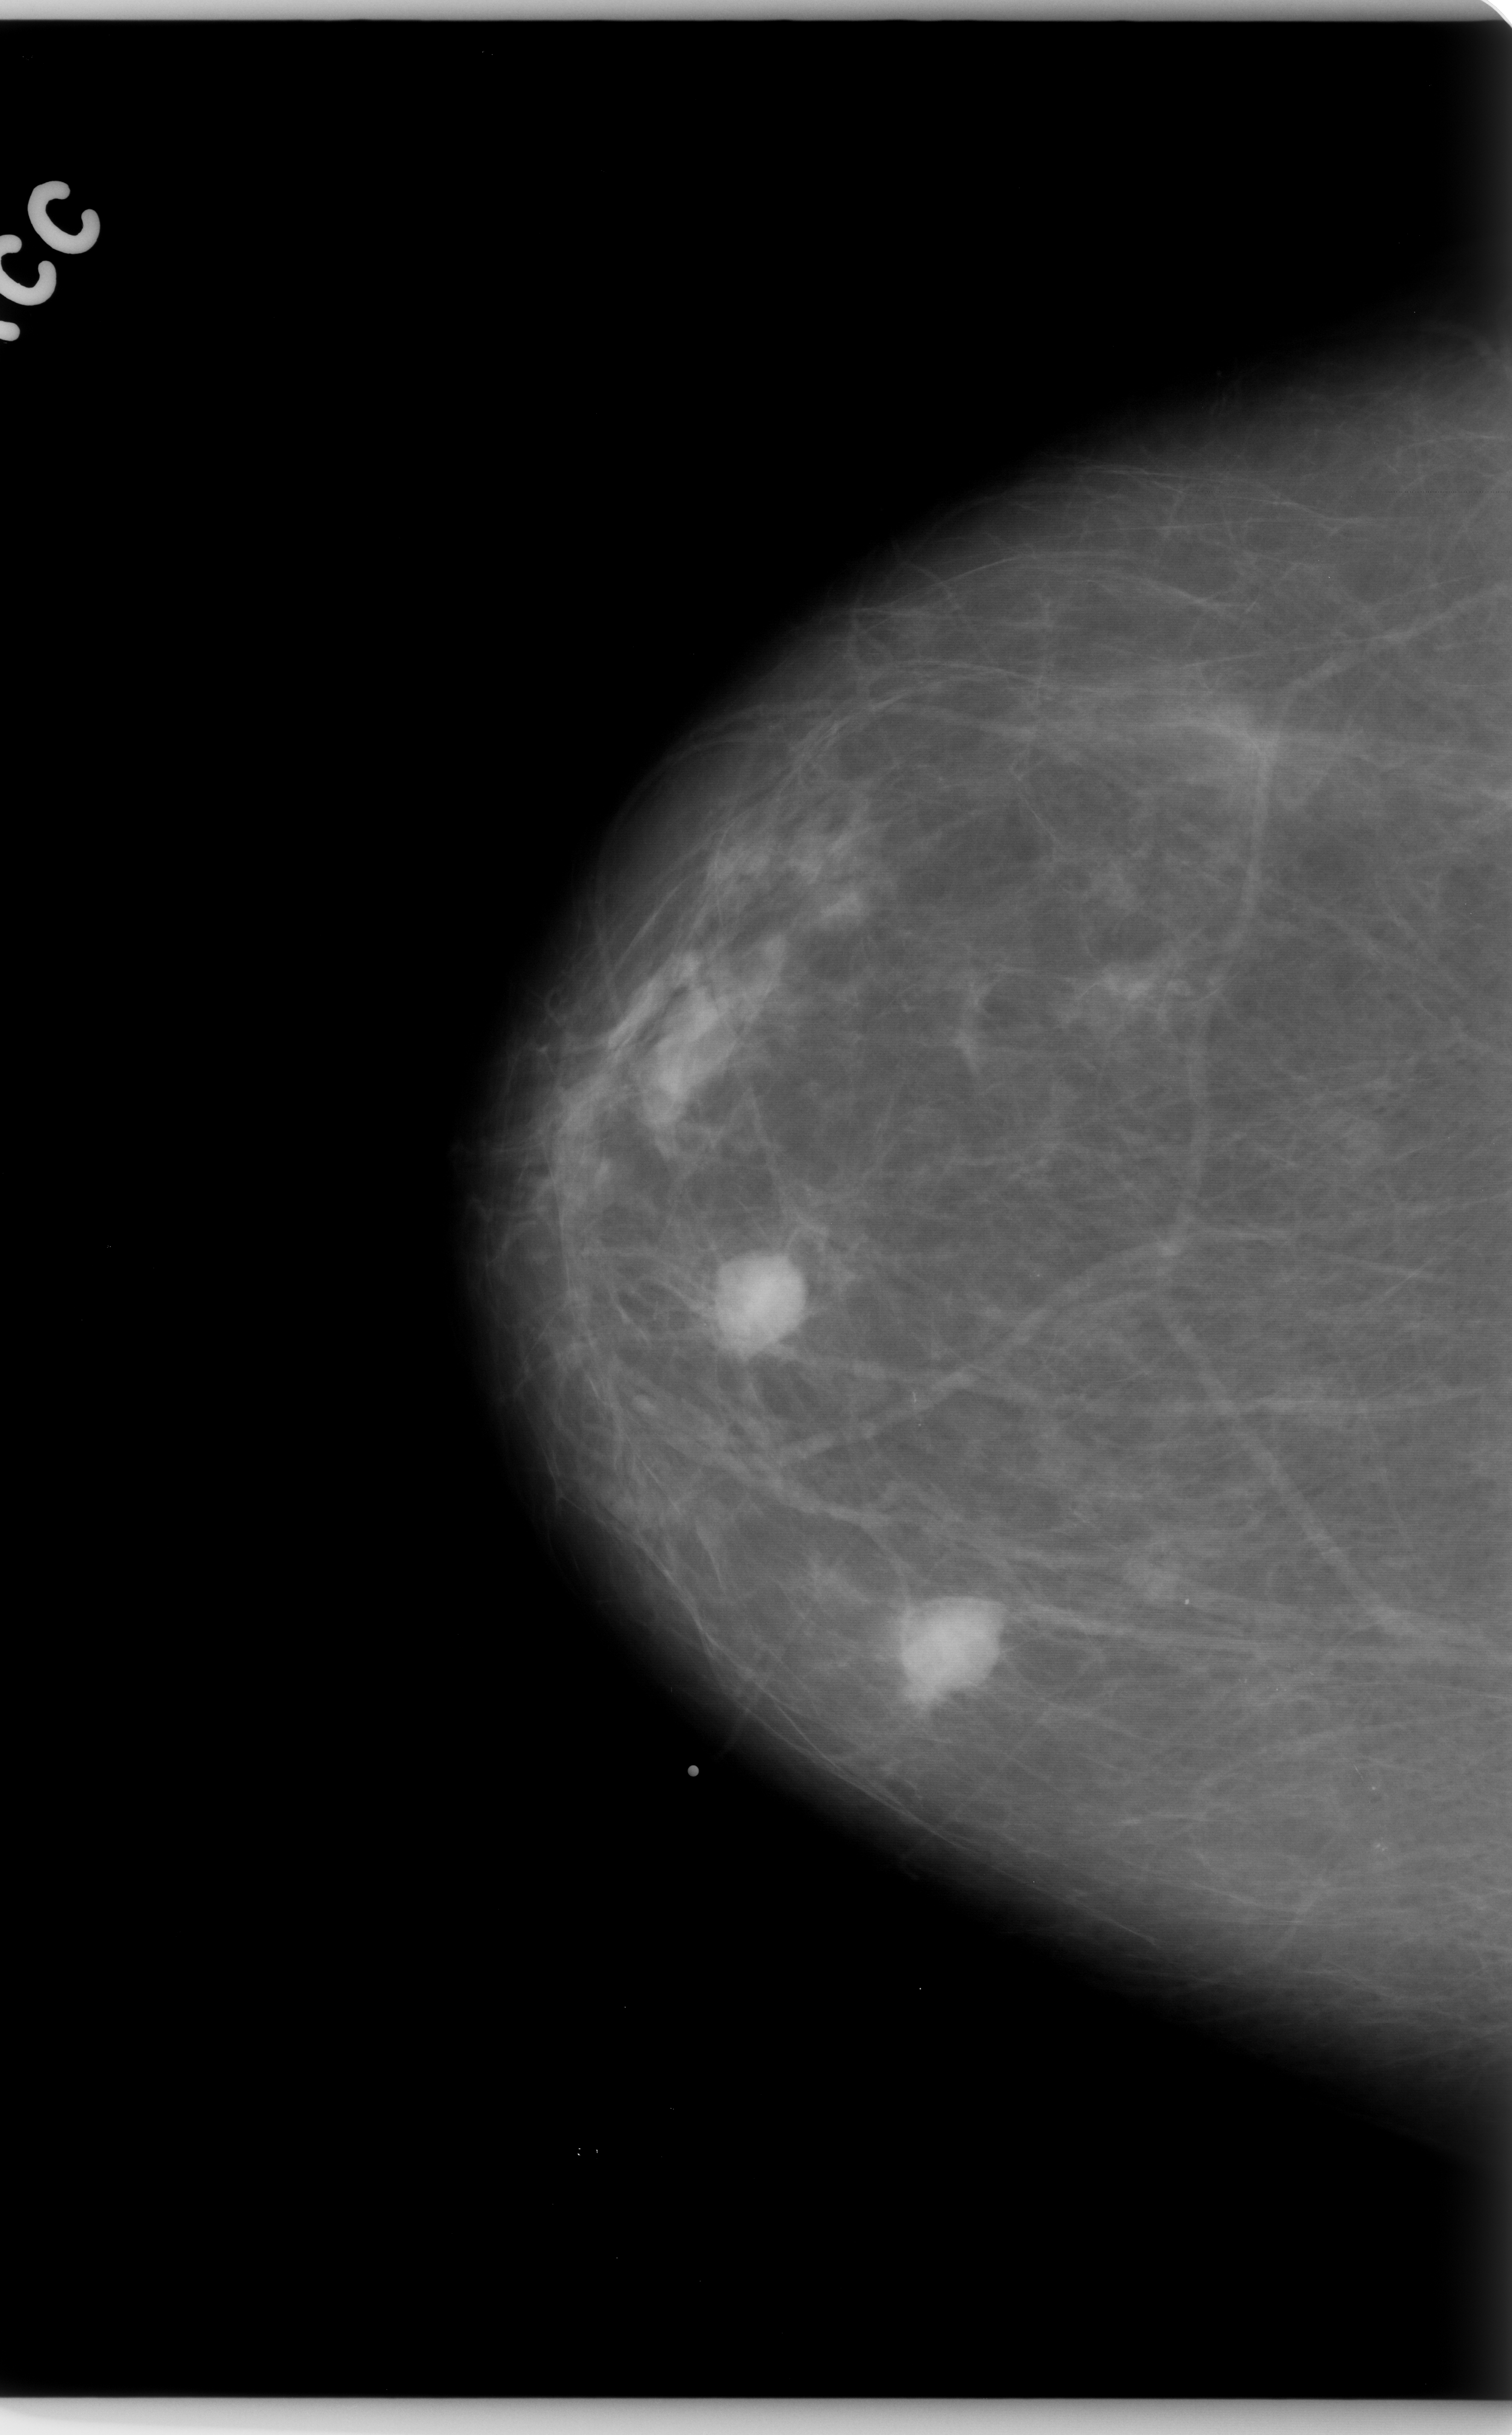
Mammogram (digitized film); right breast; CC view; breast composition: almost entirely fatty (BI-RADS density category 1 of 4).
Radiologist-marked abnormalities on this image: Finding 1 of 3: mass, shape oval, margins circumscribed; BI-RADS assessment category 4; subtlety rating 5 on a 1 (subtle) to 5 (obvious) scale; pathology result (as recorded, not read from the image): benign. Finding 2 of 3: mass, shape oval, margins microlobulated; BI-RADS assessment category 4; subtlety rating 5 on a 1 (subtle) to 5 (obvious) scale; pathology (as recorded): malignant. Finding 3 of 3: mass, shape oval, margins microlobulated; BI-RADS assessment category 4; subtlety rating 5 on a 1 (subtle) to 5 (obvious) scale; pathology (as recorded): malignant.